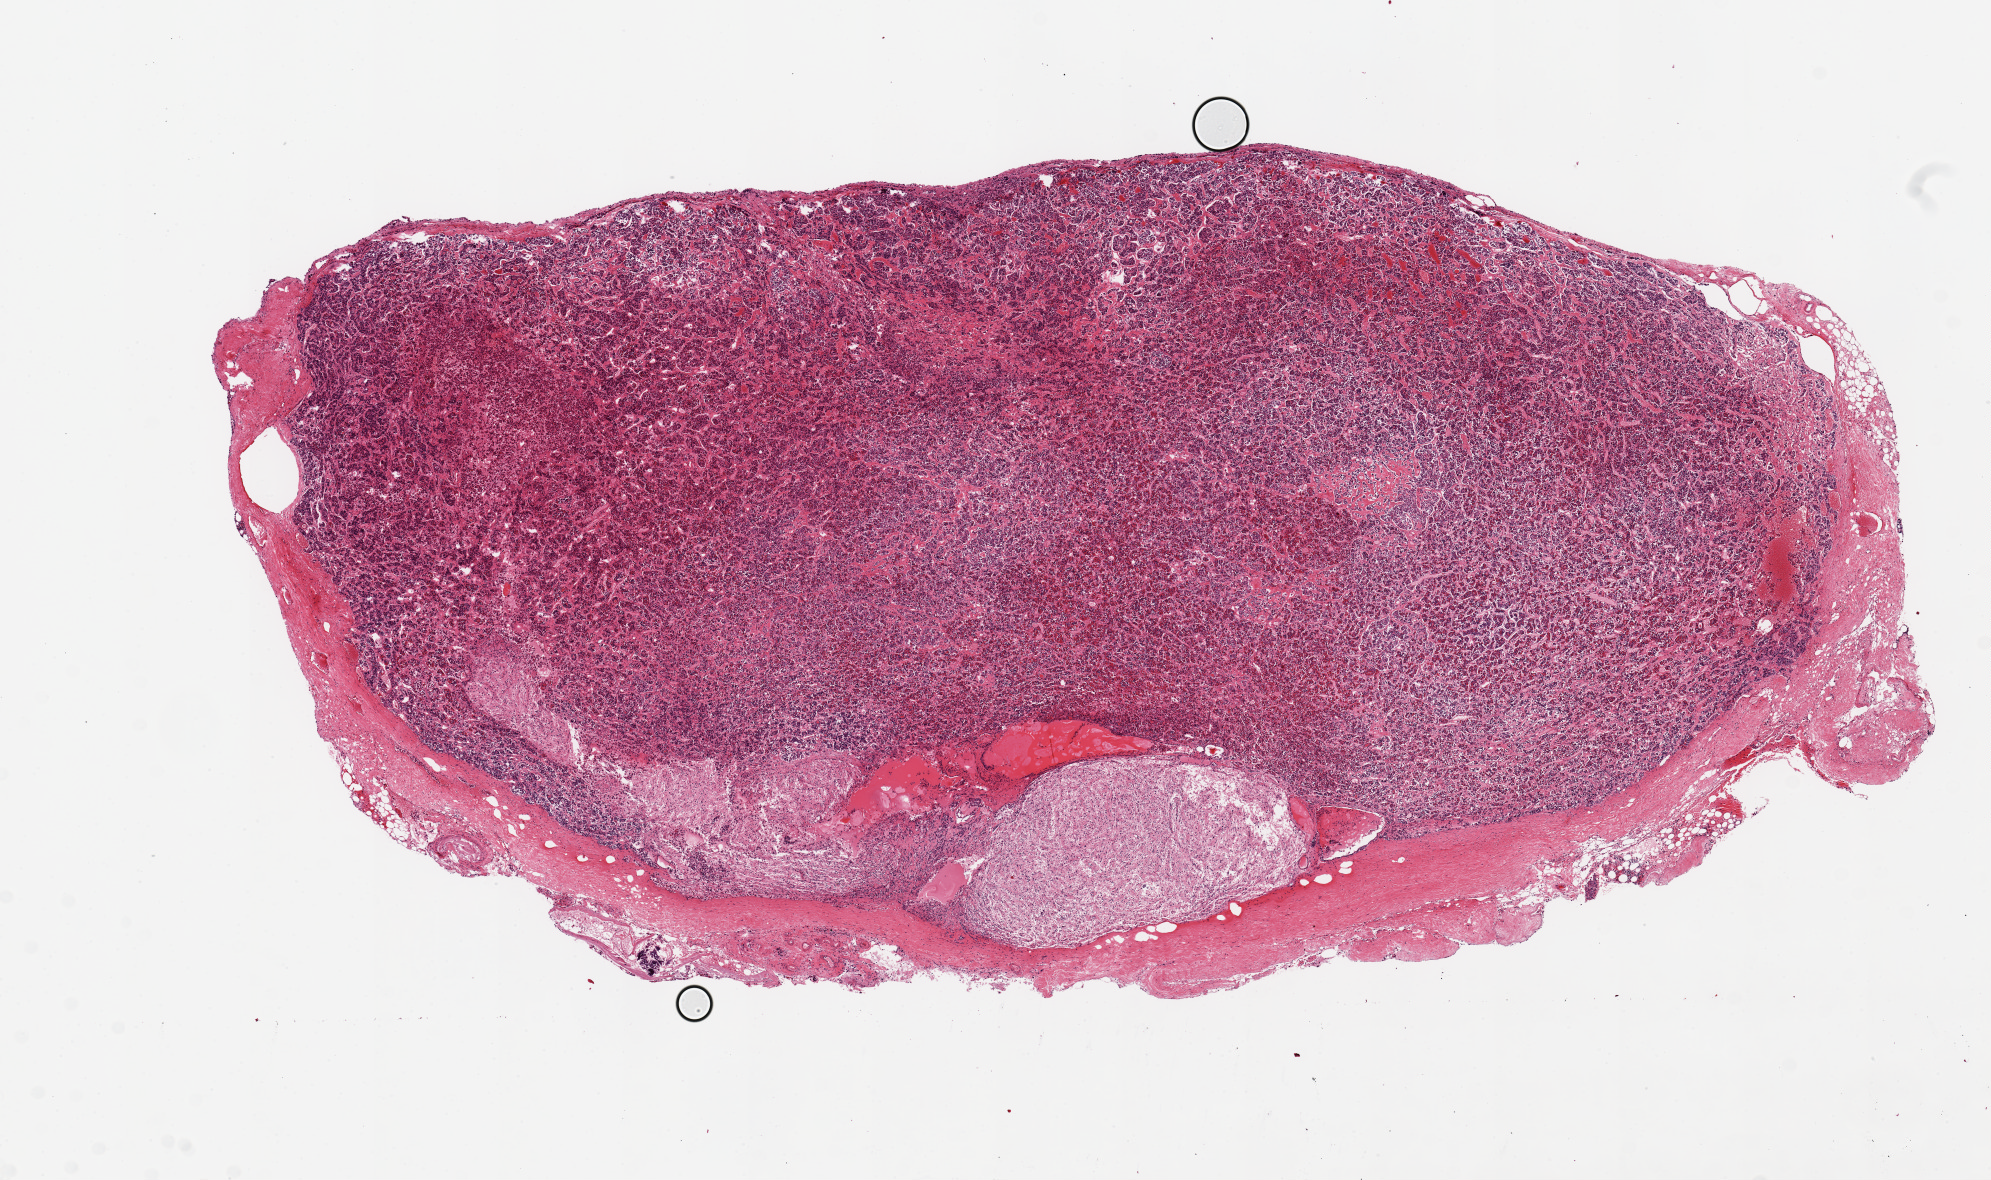
Digitized hematoxylin and eosin (H&E)-stained section, low-resolution overview of the scanned area, about 15.8 x 9.3 mm (acquisition: 20x scan). PAXgene-fixed, paraffin-embedded tissue. Section of pituitary (target tissue). Tissue donor sample. Donor sex: male.
* pathologist's review note for this sample: 1 piece, 14x7mm; ~10% is posterior pituitary